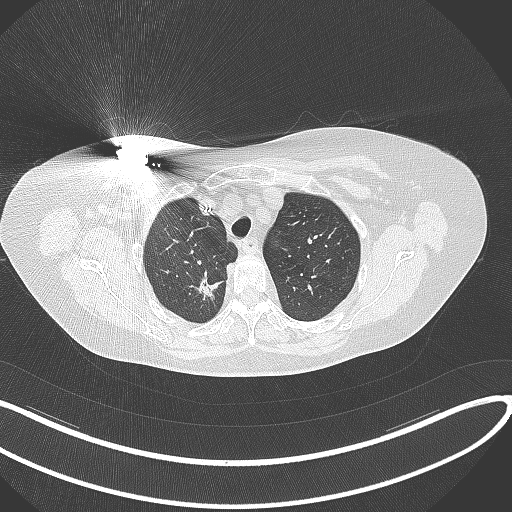
Chest CT, one axial slice; position 271 of 316 along the scan axis; reconstruction kernel B70f; lung window (W 1500 / L -600 HU); 1 mm slice thickness; 512 × 512 image matrix, field of view 400 × 400 mm. Patient: female, 72 years. Case-level facts recorded for this patient, not image findings: clinical TNM (as recorded): T1c N0 M0.
Structures marked on this image (rectangle marked by the reading radiologist):
- lung tumour (recorded histology: adenocarcinoma): bounding box (x1, y1, x2, y2) in pixels: (187, 264, 222, 303)